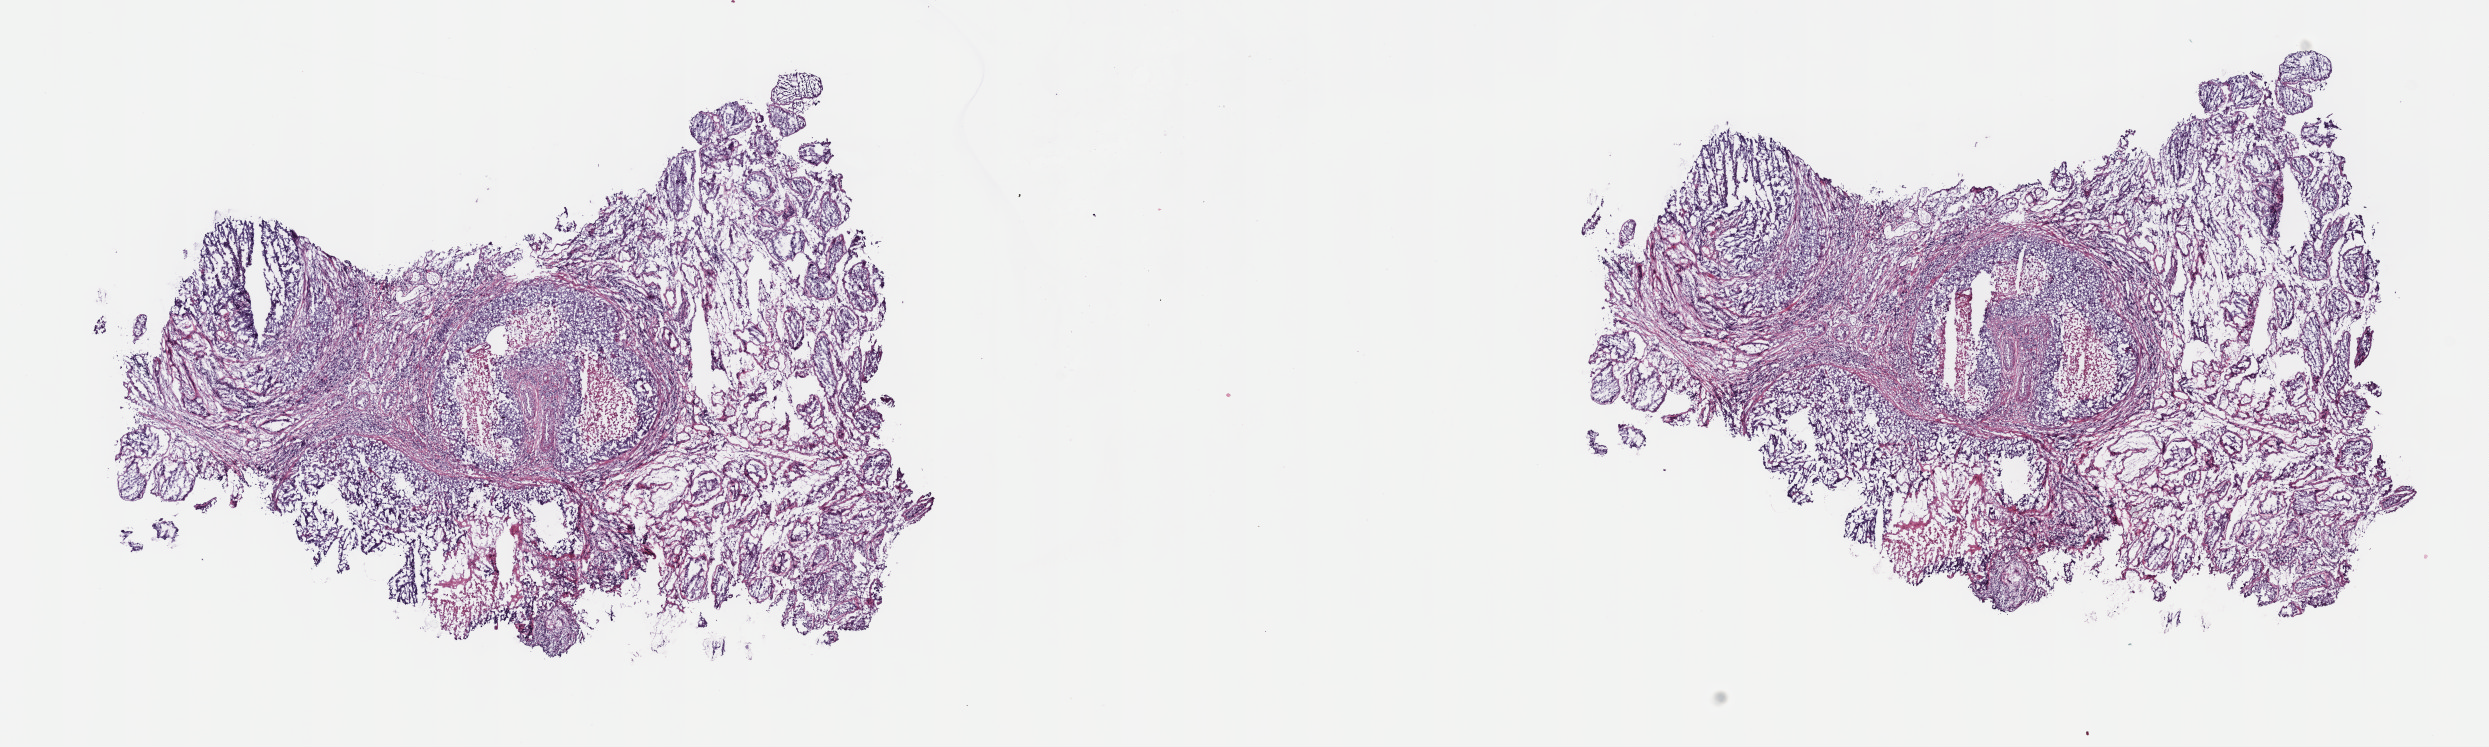
H&E whole-slide image, low-resolution overview of the scanned area, about 20.1 x 6.0 mm (acquisition: 40x scan). Frozen section from the top of the tissue portion. Sample: primary tumour, testis. Male, age 35 years at initial diagnosis. Composition of this section per pathologist review: tumour cells 45%, tumour nuclei 70%.
Diagnosis: Embryonal carcinoma, NOS.